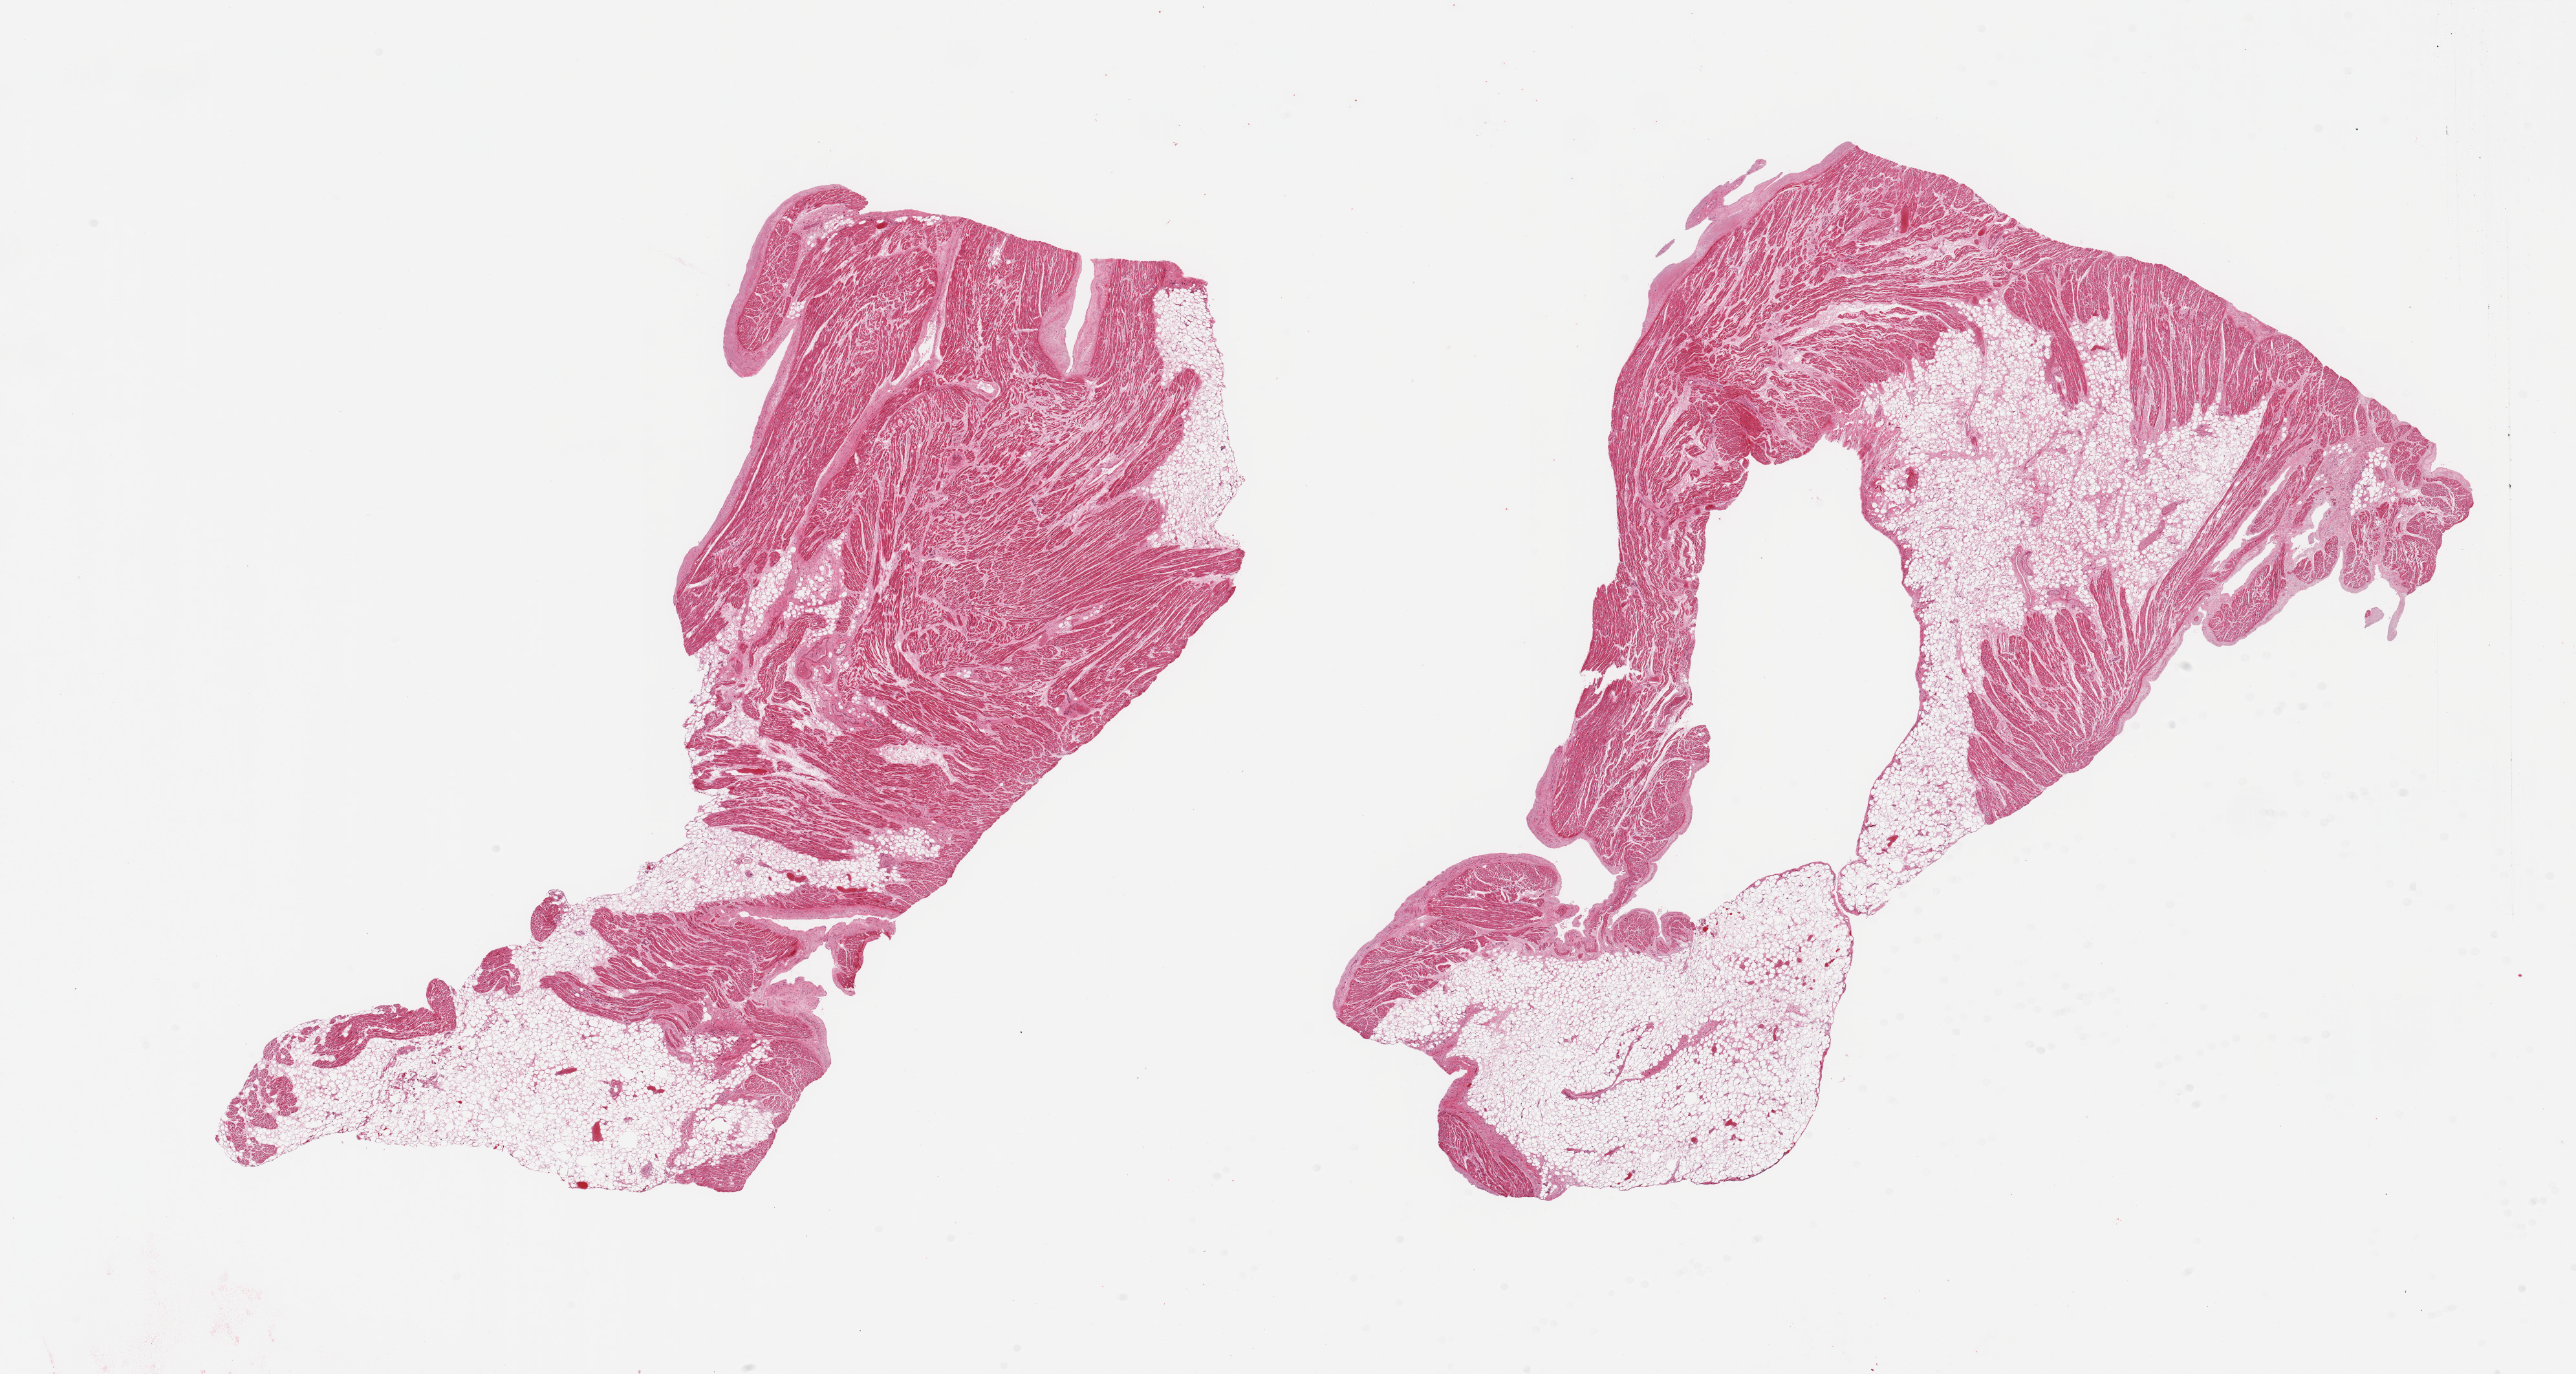
Digitized haematoxylin and eosin-stained section — whole scanned area (about 31.5 x 16.8 mm, slide scanned at 20x) shown as a low-resolution overview, PAXgene-fixed, paraffin-embedded tissue, target tissue: auricular appendage, tissue donor sample. Male donor.
Reviewer comment on this tissue sample: 2 pieces, no abnormalities, ~30% total tssue is fat.